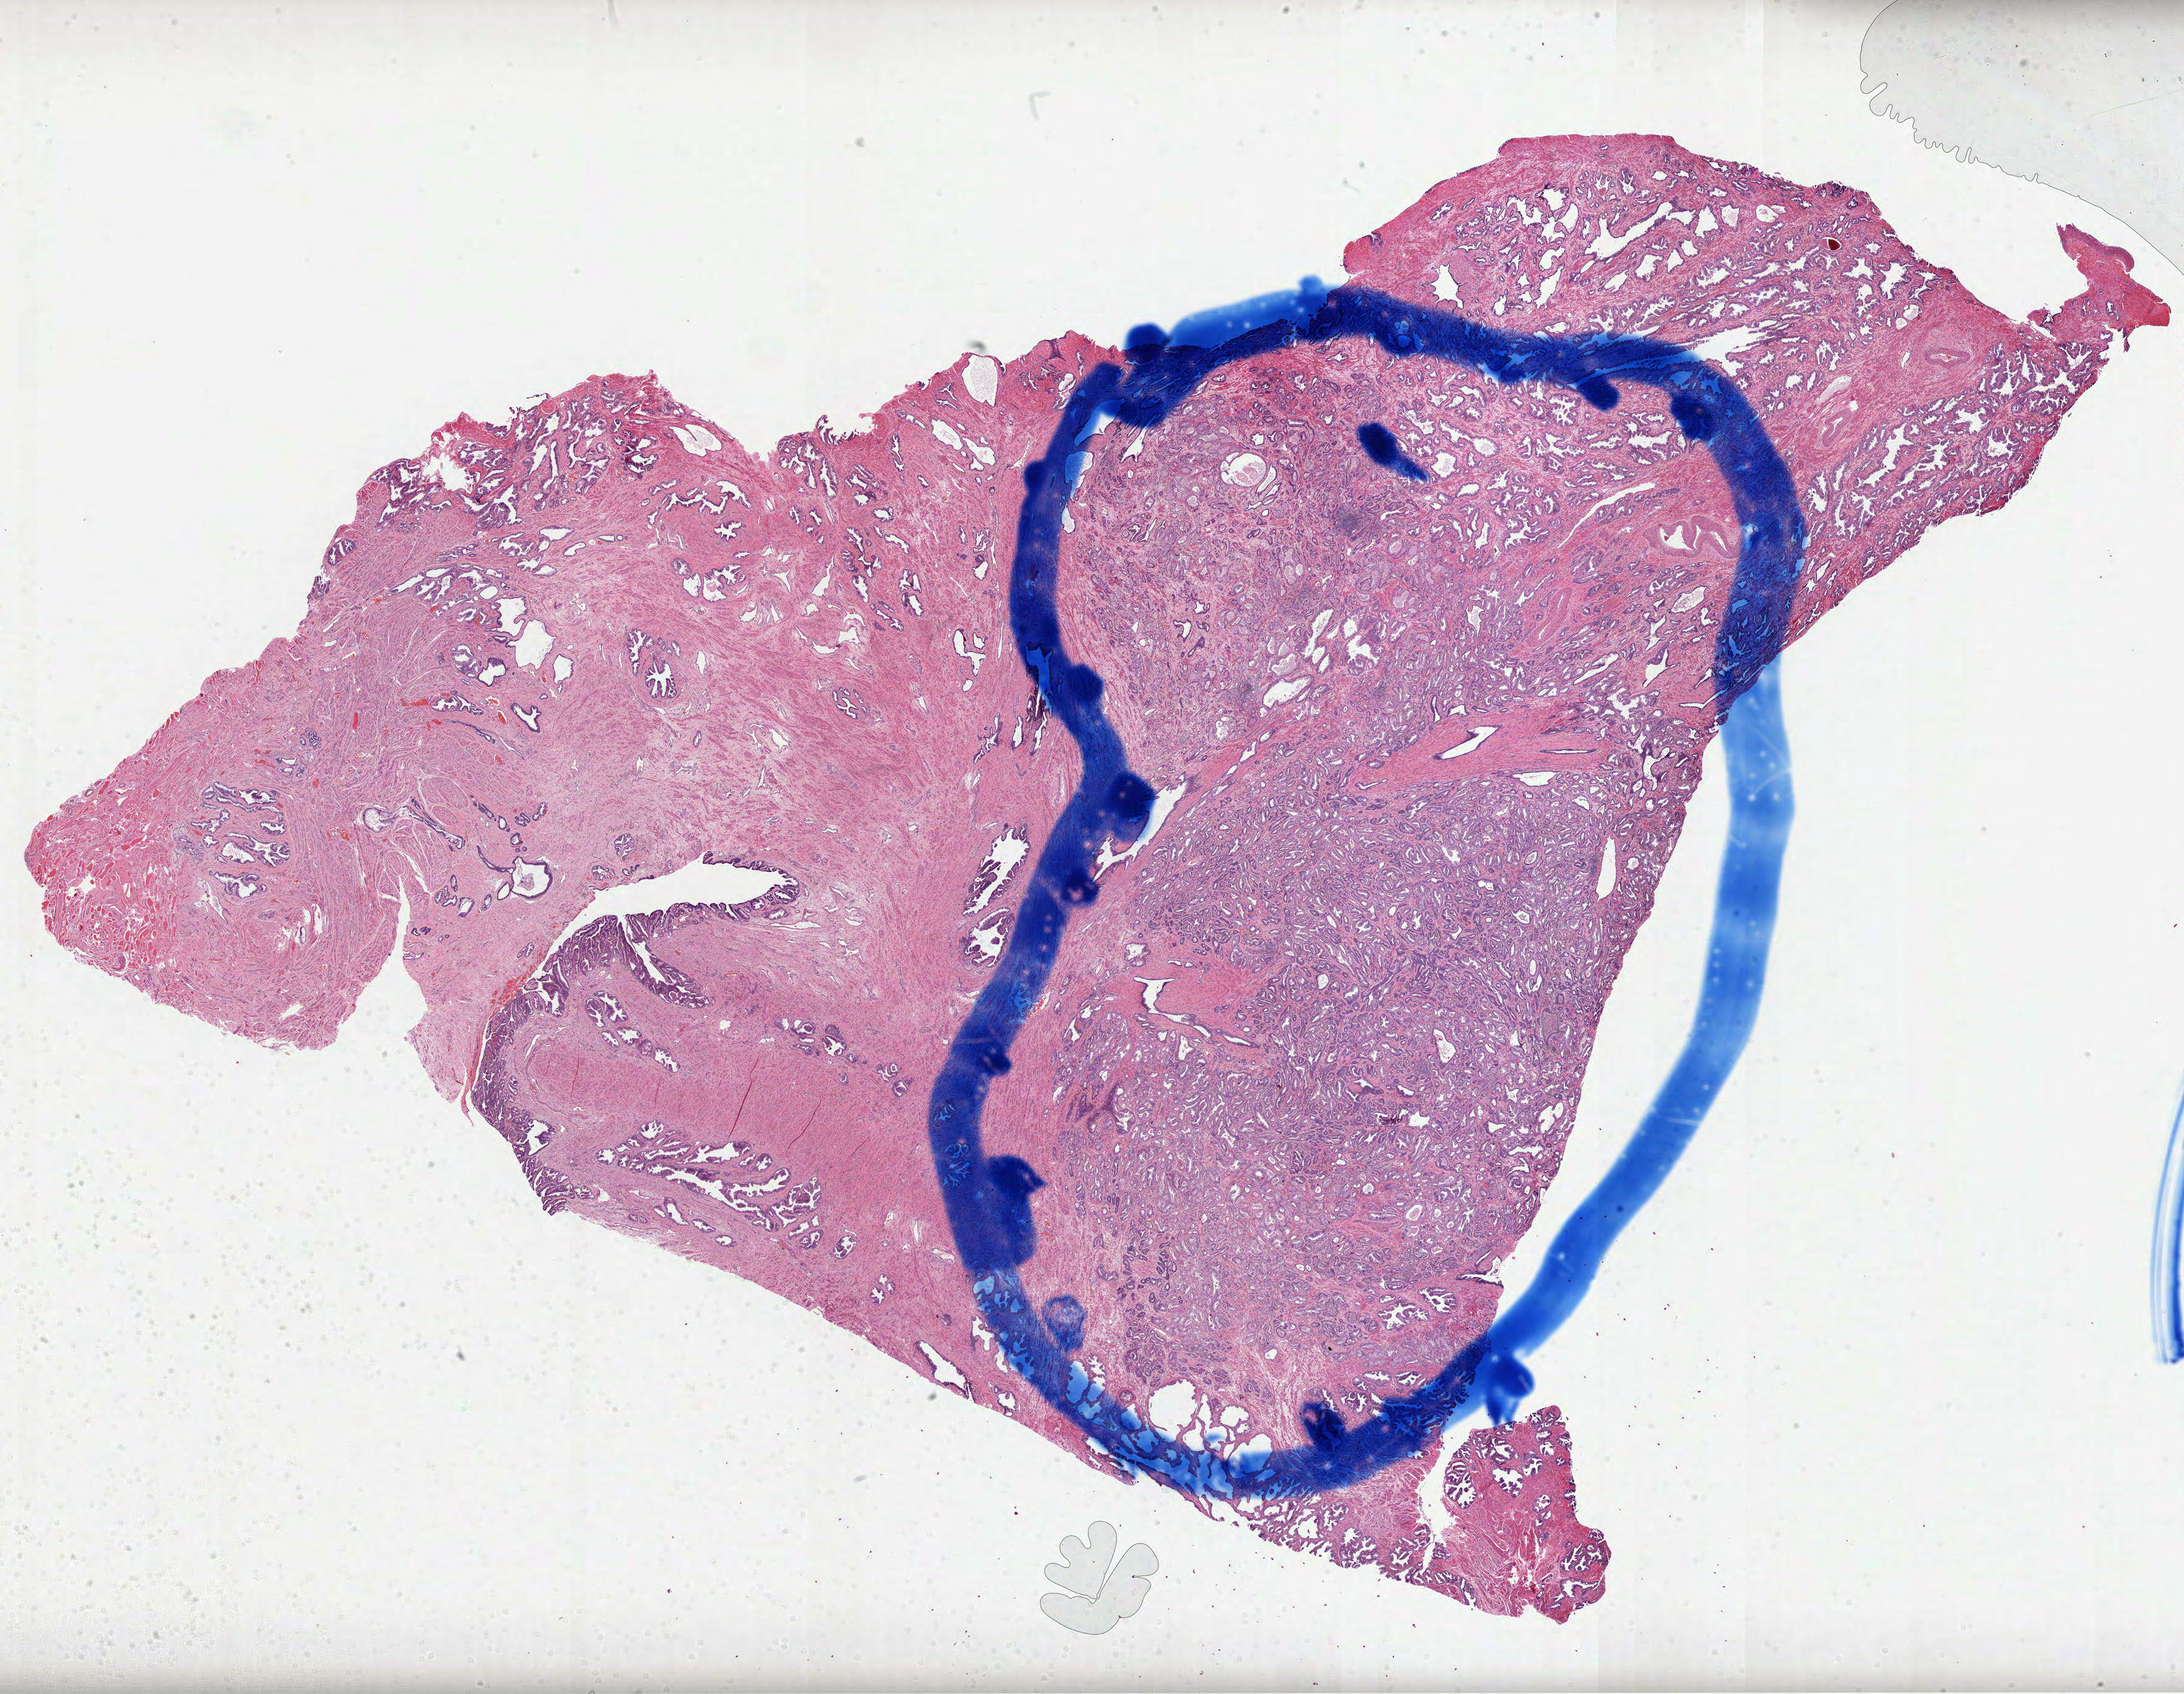
H&E-stained whole-slide image — shown as a low-resolution overview of the whole scanned area (about 28.8 x 22.3 mm, acquisition: 40x scan). Formalin-fixed paraffin-embedded (FFPE) diagnostic section. Sample: primary tumour, prostate. Male patient; age at initial diagnosis 47 years. Gleason score: 7 (3+4).
- histologic diagnosis: Acinar cell carcinoma (prostate gland)